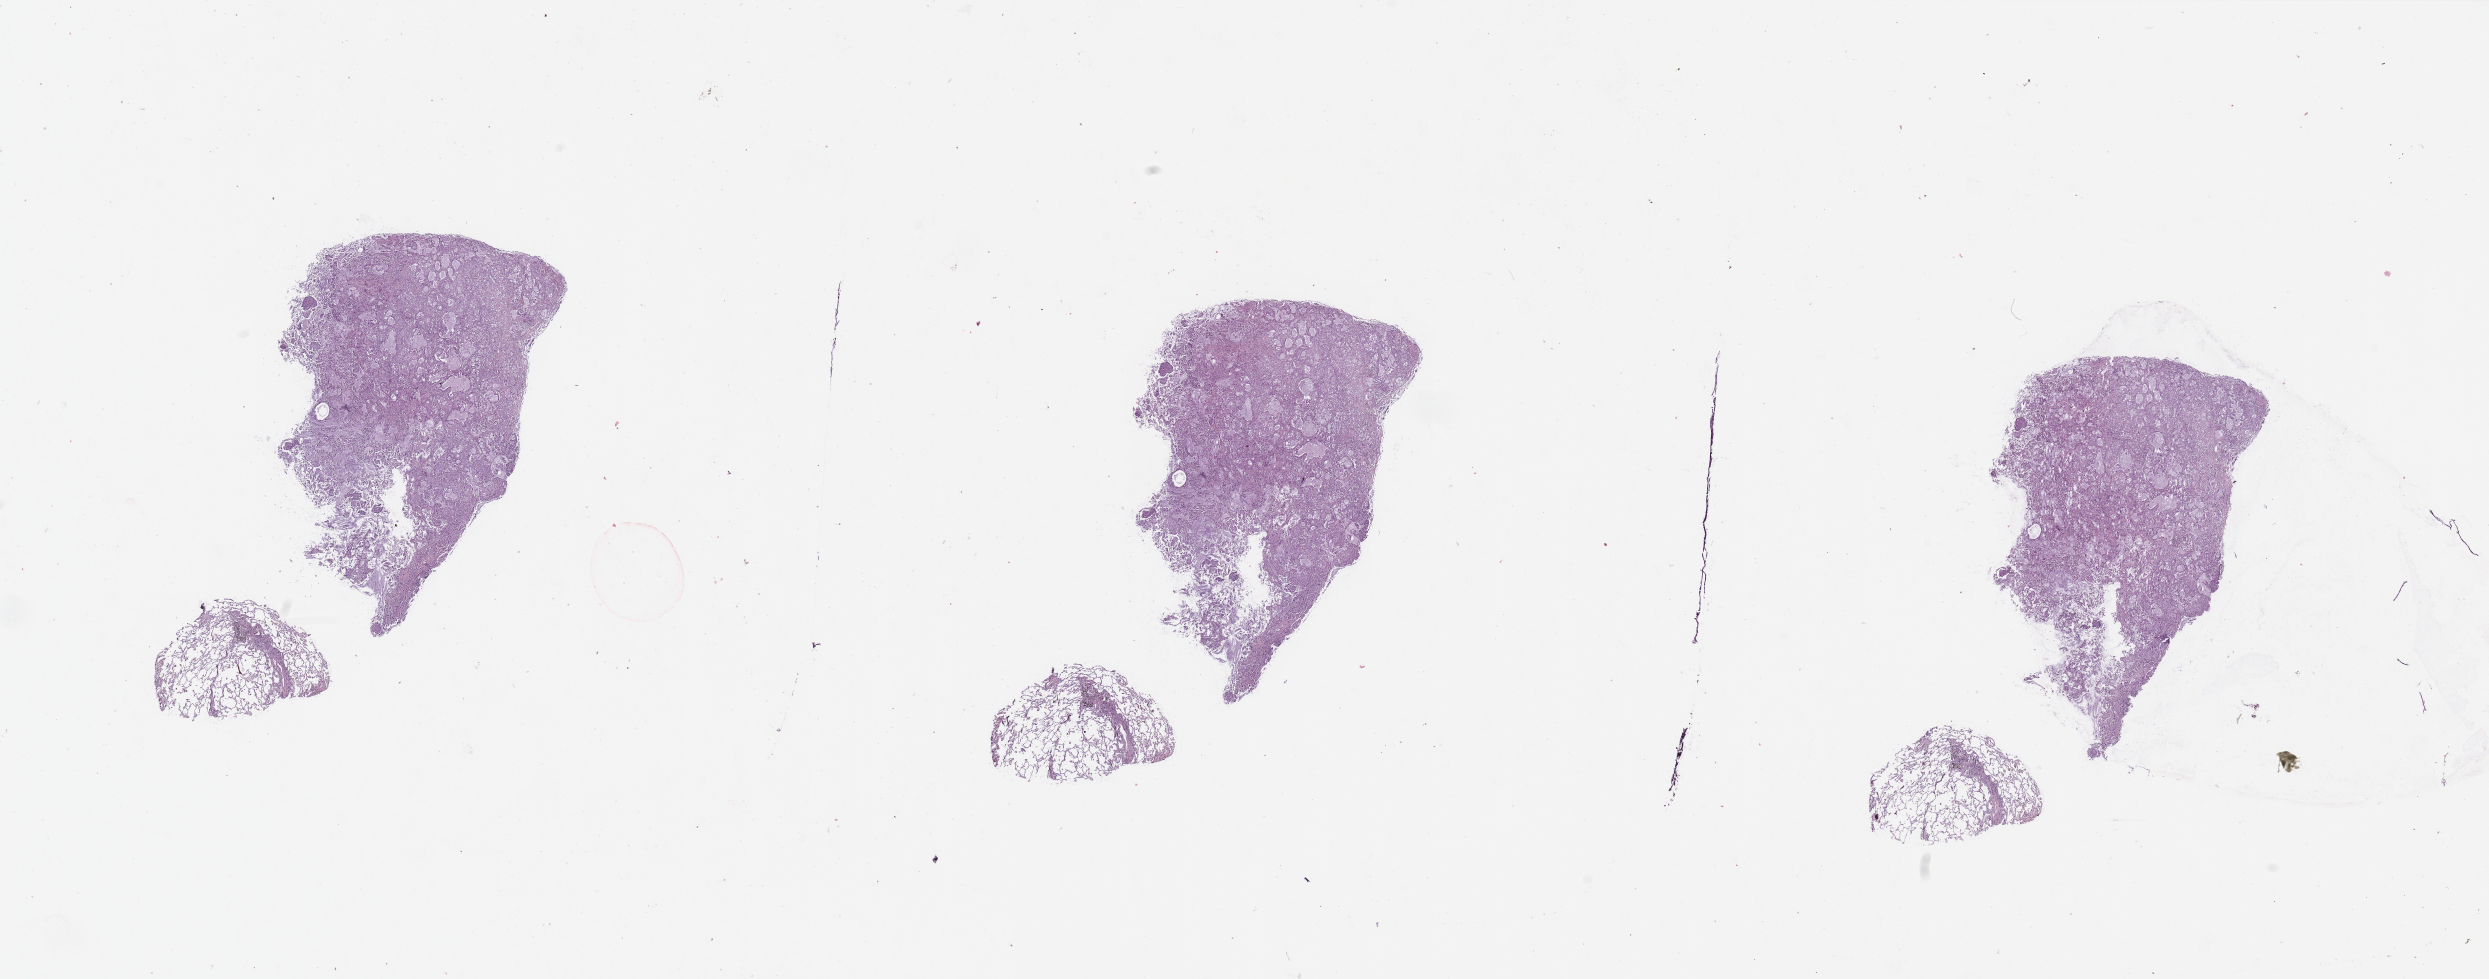
Whole-slide histology image, H&E-stained, low-resolution overview of the scanned area, about 39.4 x 15.5 mm (slide scanned at 20x). Tumour tissue sample, lung. Male, 51 y/o. Histologic grade: G2 (moderately differentiated).
Diagnosis: Adenocarcinoma, NOS. AJCC pathologic stage: IIIA.